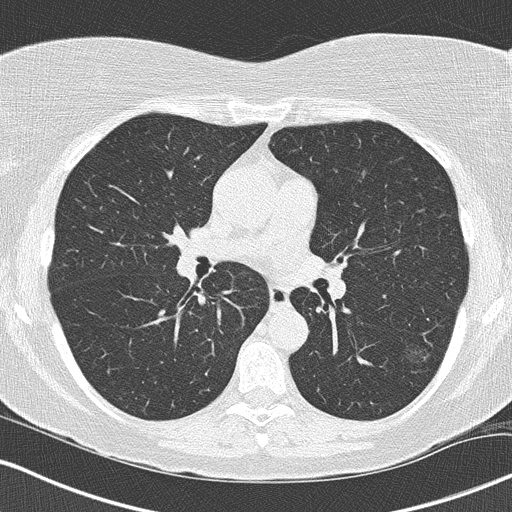
Chest CT (low-dose screening protocol), one axial image. Third annual screen. Lung window (W 1500 / L -600 HU). 2 mm slice thickness. Lung (sharp) reconstruction kernel (B50f). Slice 77 of 160 in the series. 512 × 512 image matrix. Female, age 57 years at enrolment.
- Expert-annotated lung lesion, bounding box (x1, y1, x2, y2) in pixels: (388, 327, 452, 378).
- The screening reader recorded 5 non-calcified nodules or masses ≥4 mm on this exam (left lower lobe, right upper lobe, right lower lobe, right upper lobe); which of them this box marks is not recorded.
- Participant outcome: lung cancer diagnosed 51 days after this screen — bronchiolo-alveolar adenocarcinoma, NOS, left lower lobe, well differentiated (G1), stage IA (AJCC 6th edition), 16 mm at pathology.